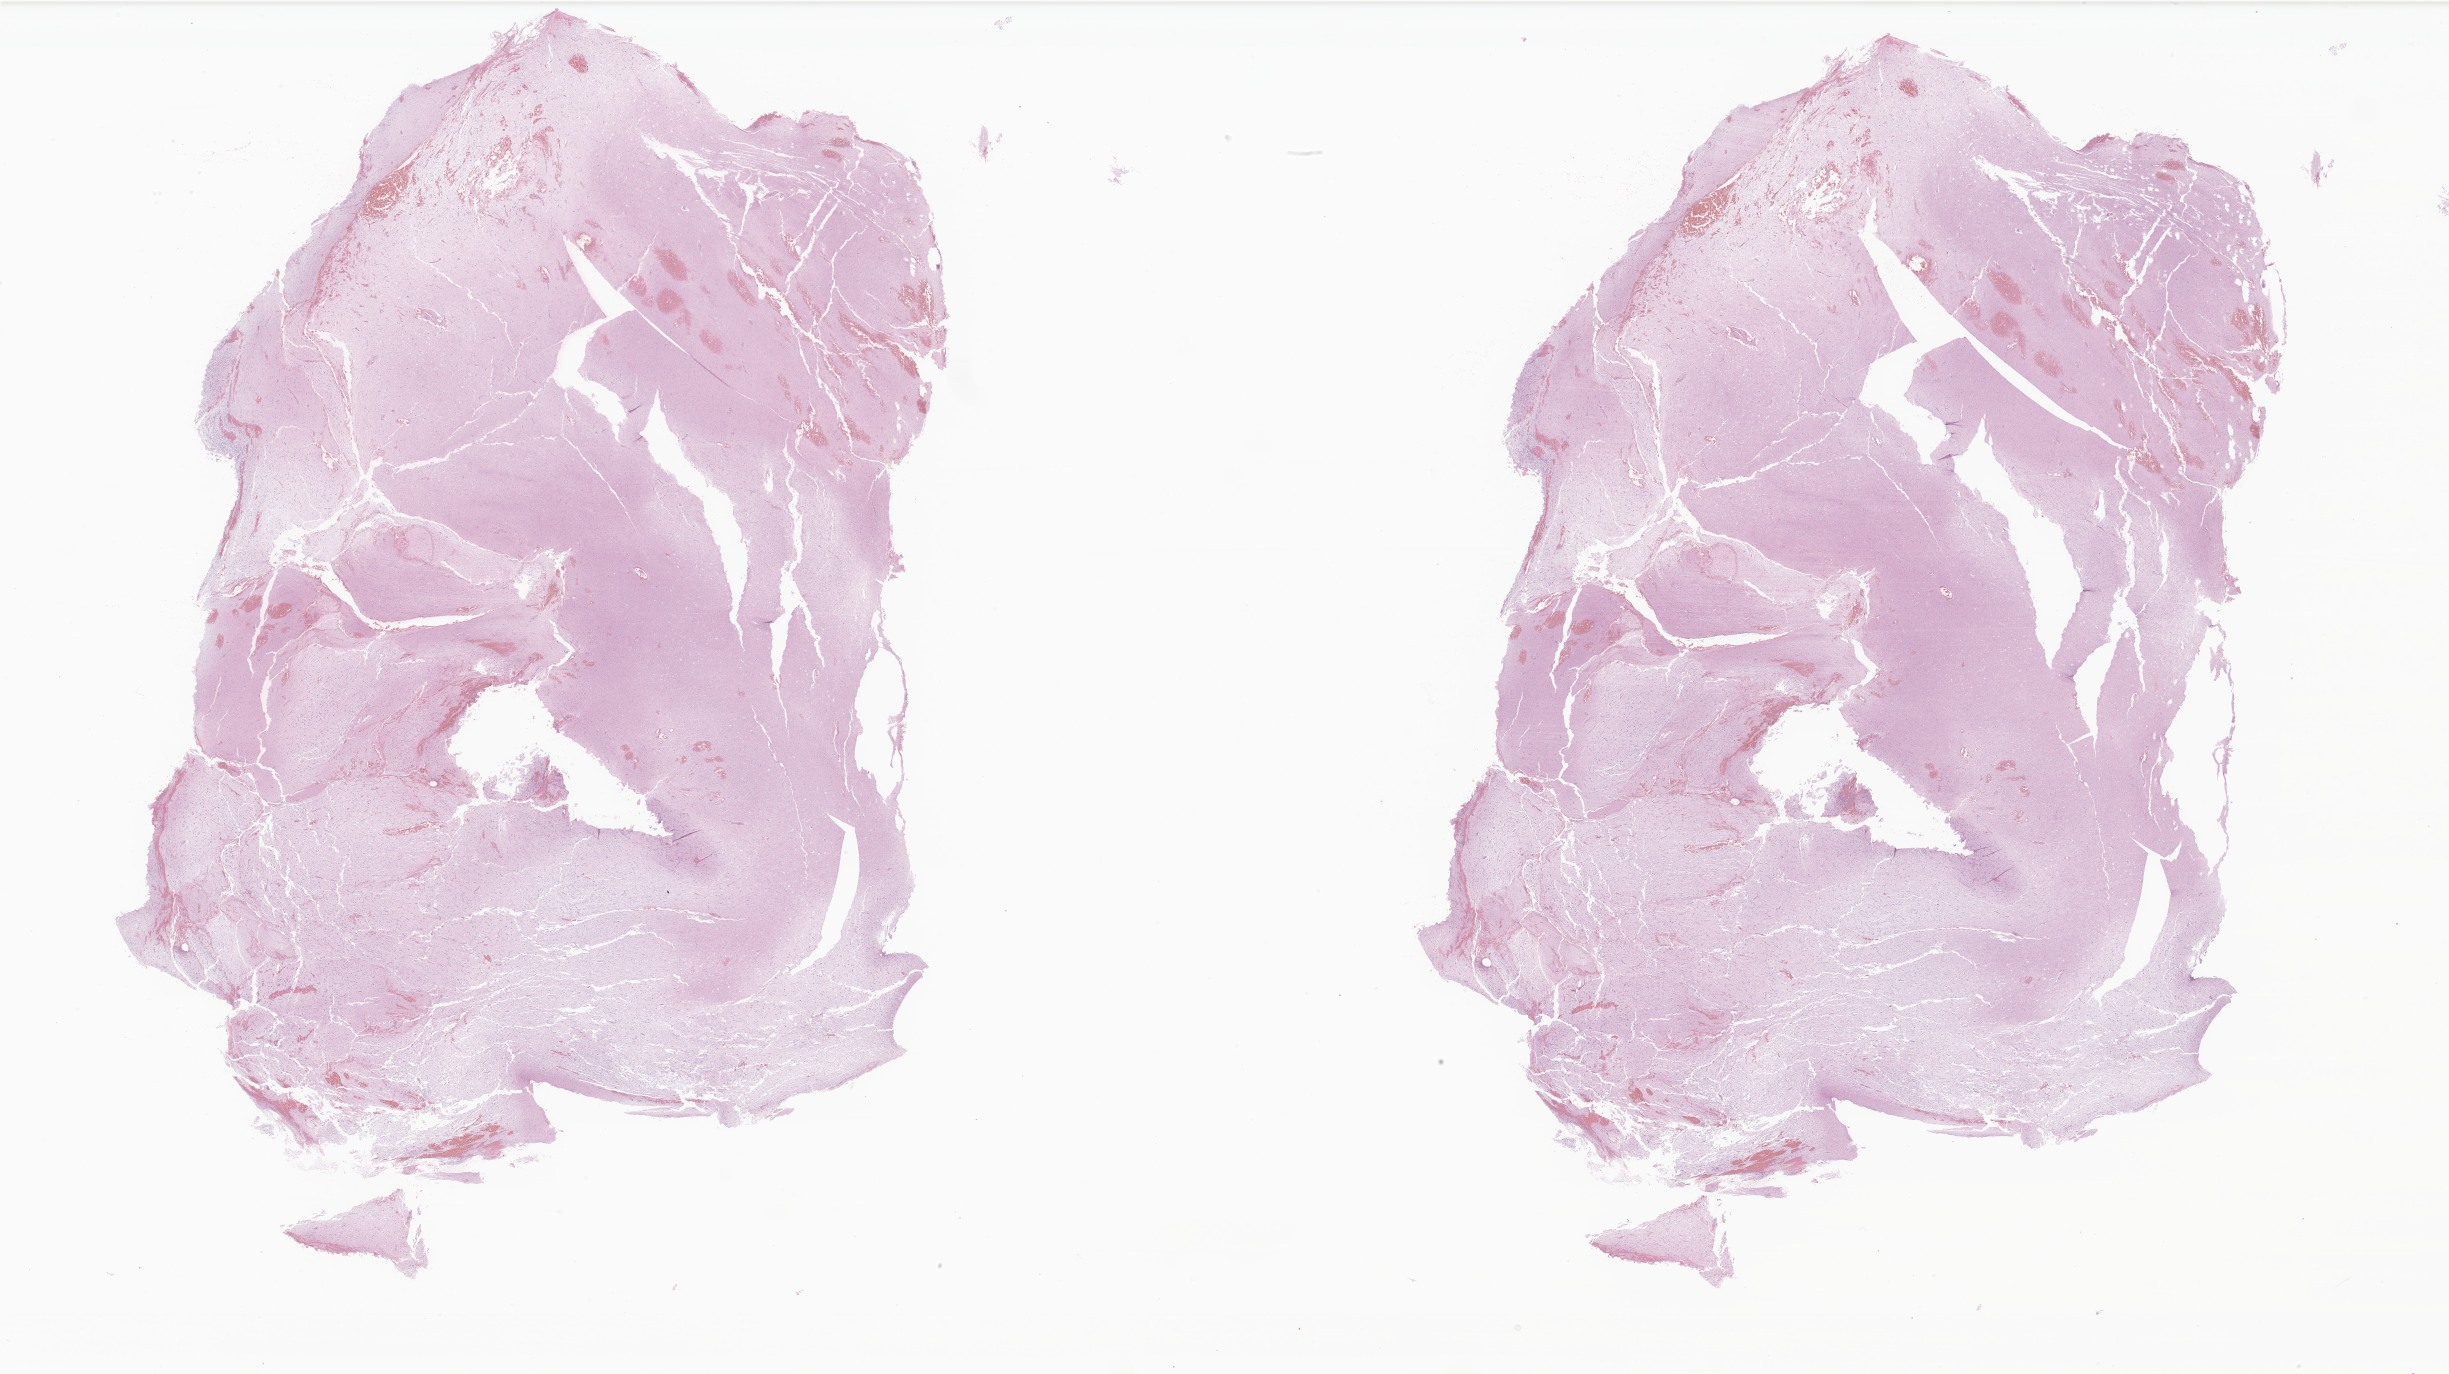
Whole-slide image, hematoxylin and eosin (H&E) stain of tumor tissue from the frontal lobe — shown as a low-resolution overview of the whole scanned area (about 41.3 x 23.2 mm); formalin-fixed paraffin-embedded section. Patient male; age 150 months (12 years 6 months).
Recorded diagnosis: Dysembryoplastic neuroepithelial tumor.